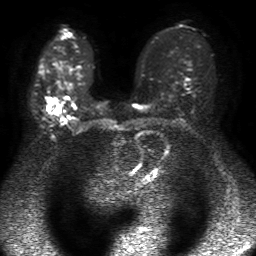
Breast MRI, one axial slice. Position 31 of 50 along the scan axis. Diffusion-weighted series; image 2 of 4 stored at this slice position (different b-values; order by instance number). 1.5 T. 4 mm slice thickness. 256 × 256 image matrix, field of view 320 × 320 mm. Female patient.
Structures marked on this image (outlined manually by an expert reader):
- tumour on diffusion-weighted imaging: box from (x=46, y=97) to (x=61, y=114) px